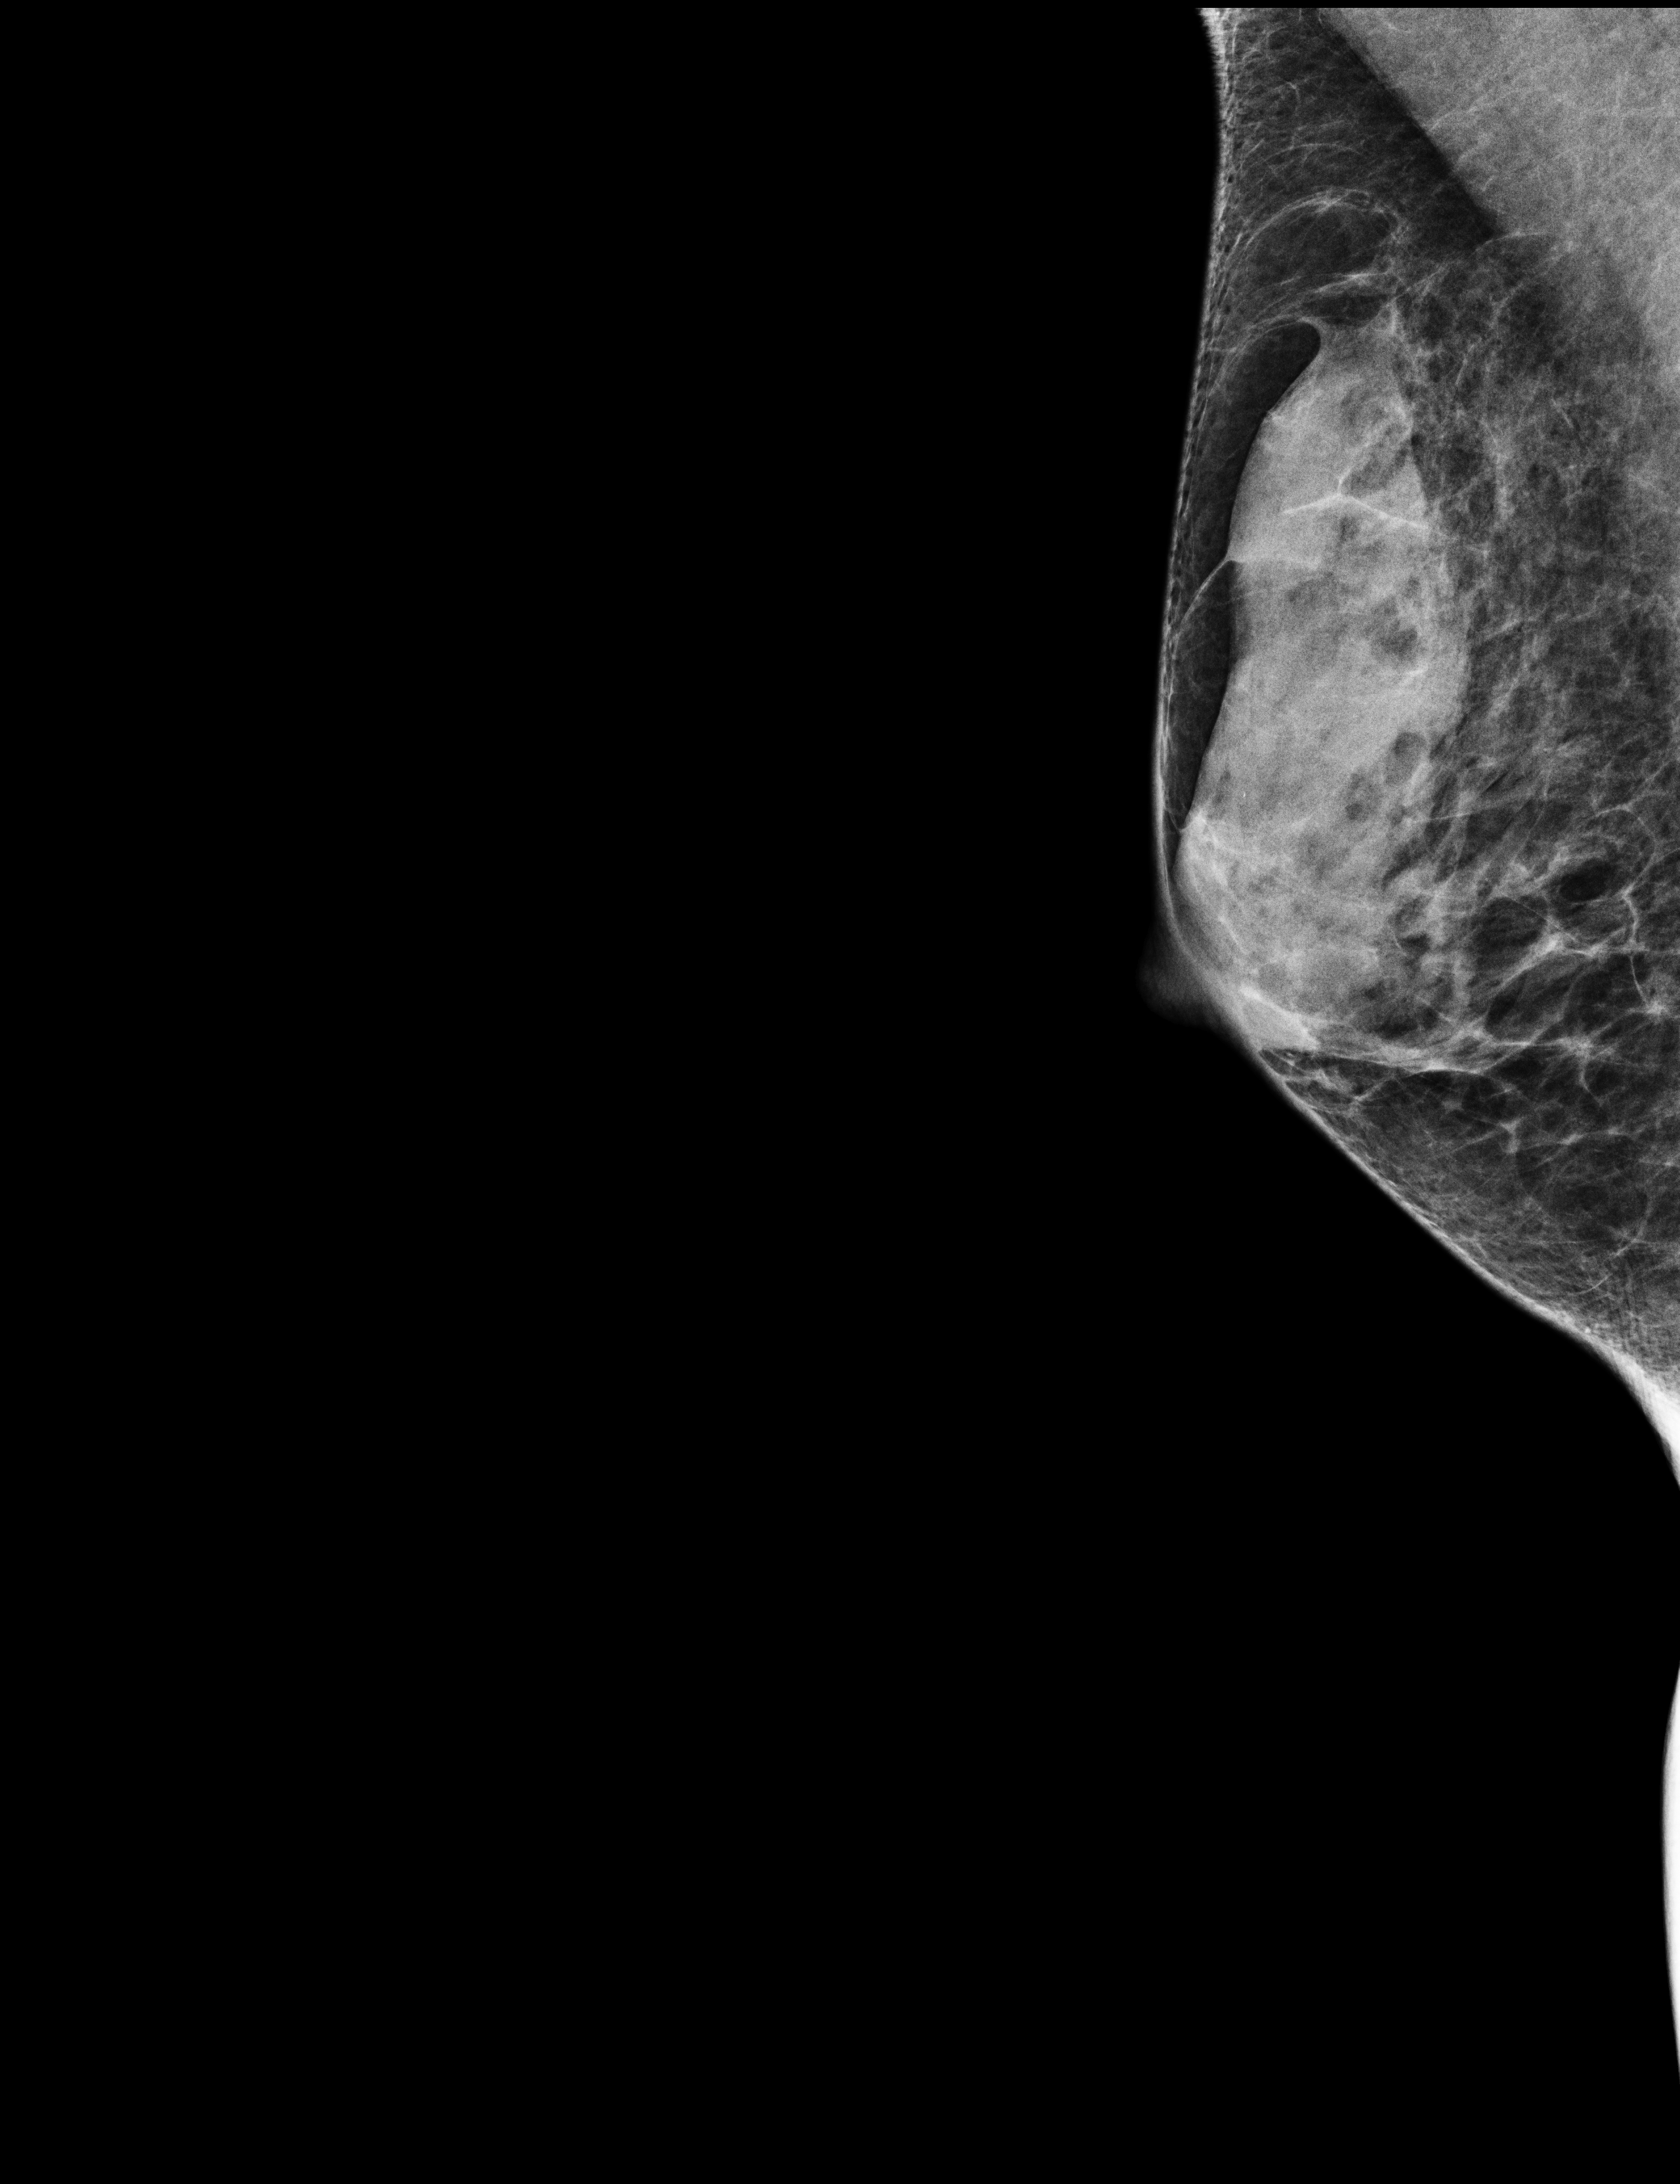
Screening examination. Female patient, age 61 years.
Image type: full-field digital mammogram. Breast: right. Projection: medio-lateral oblique projection.